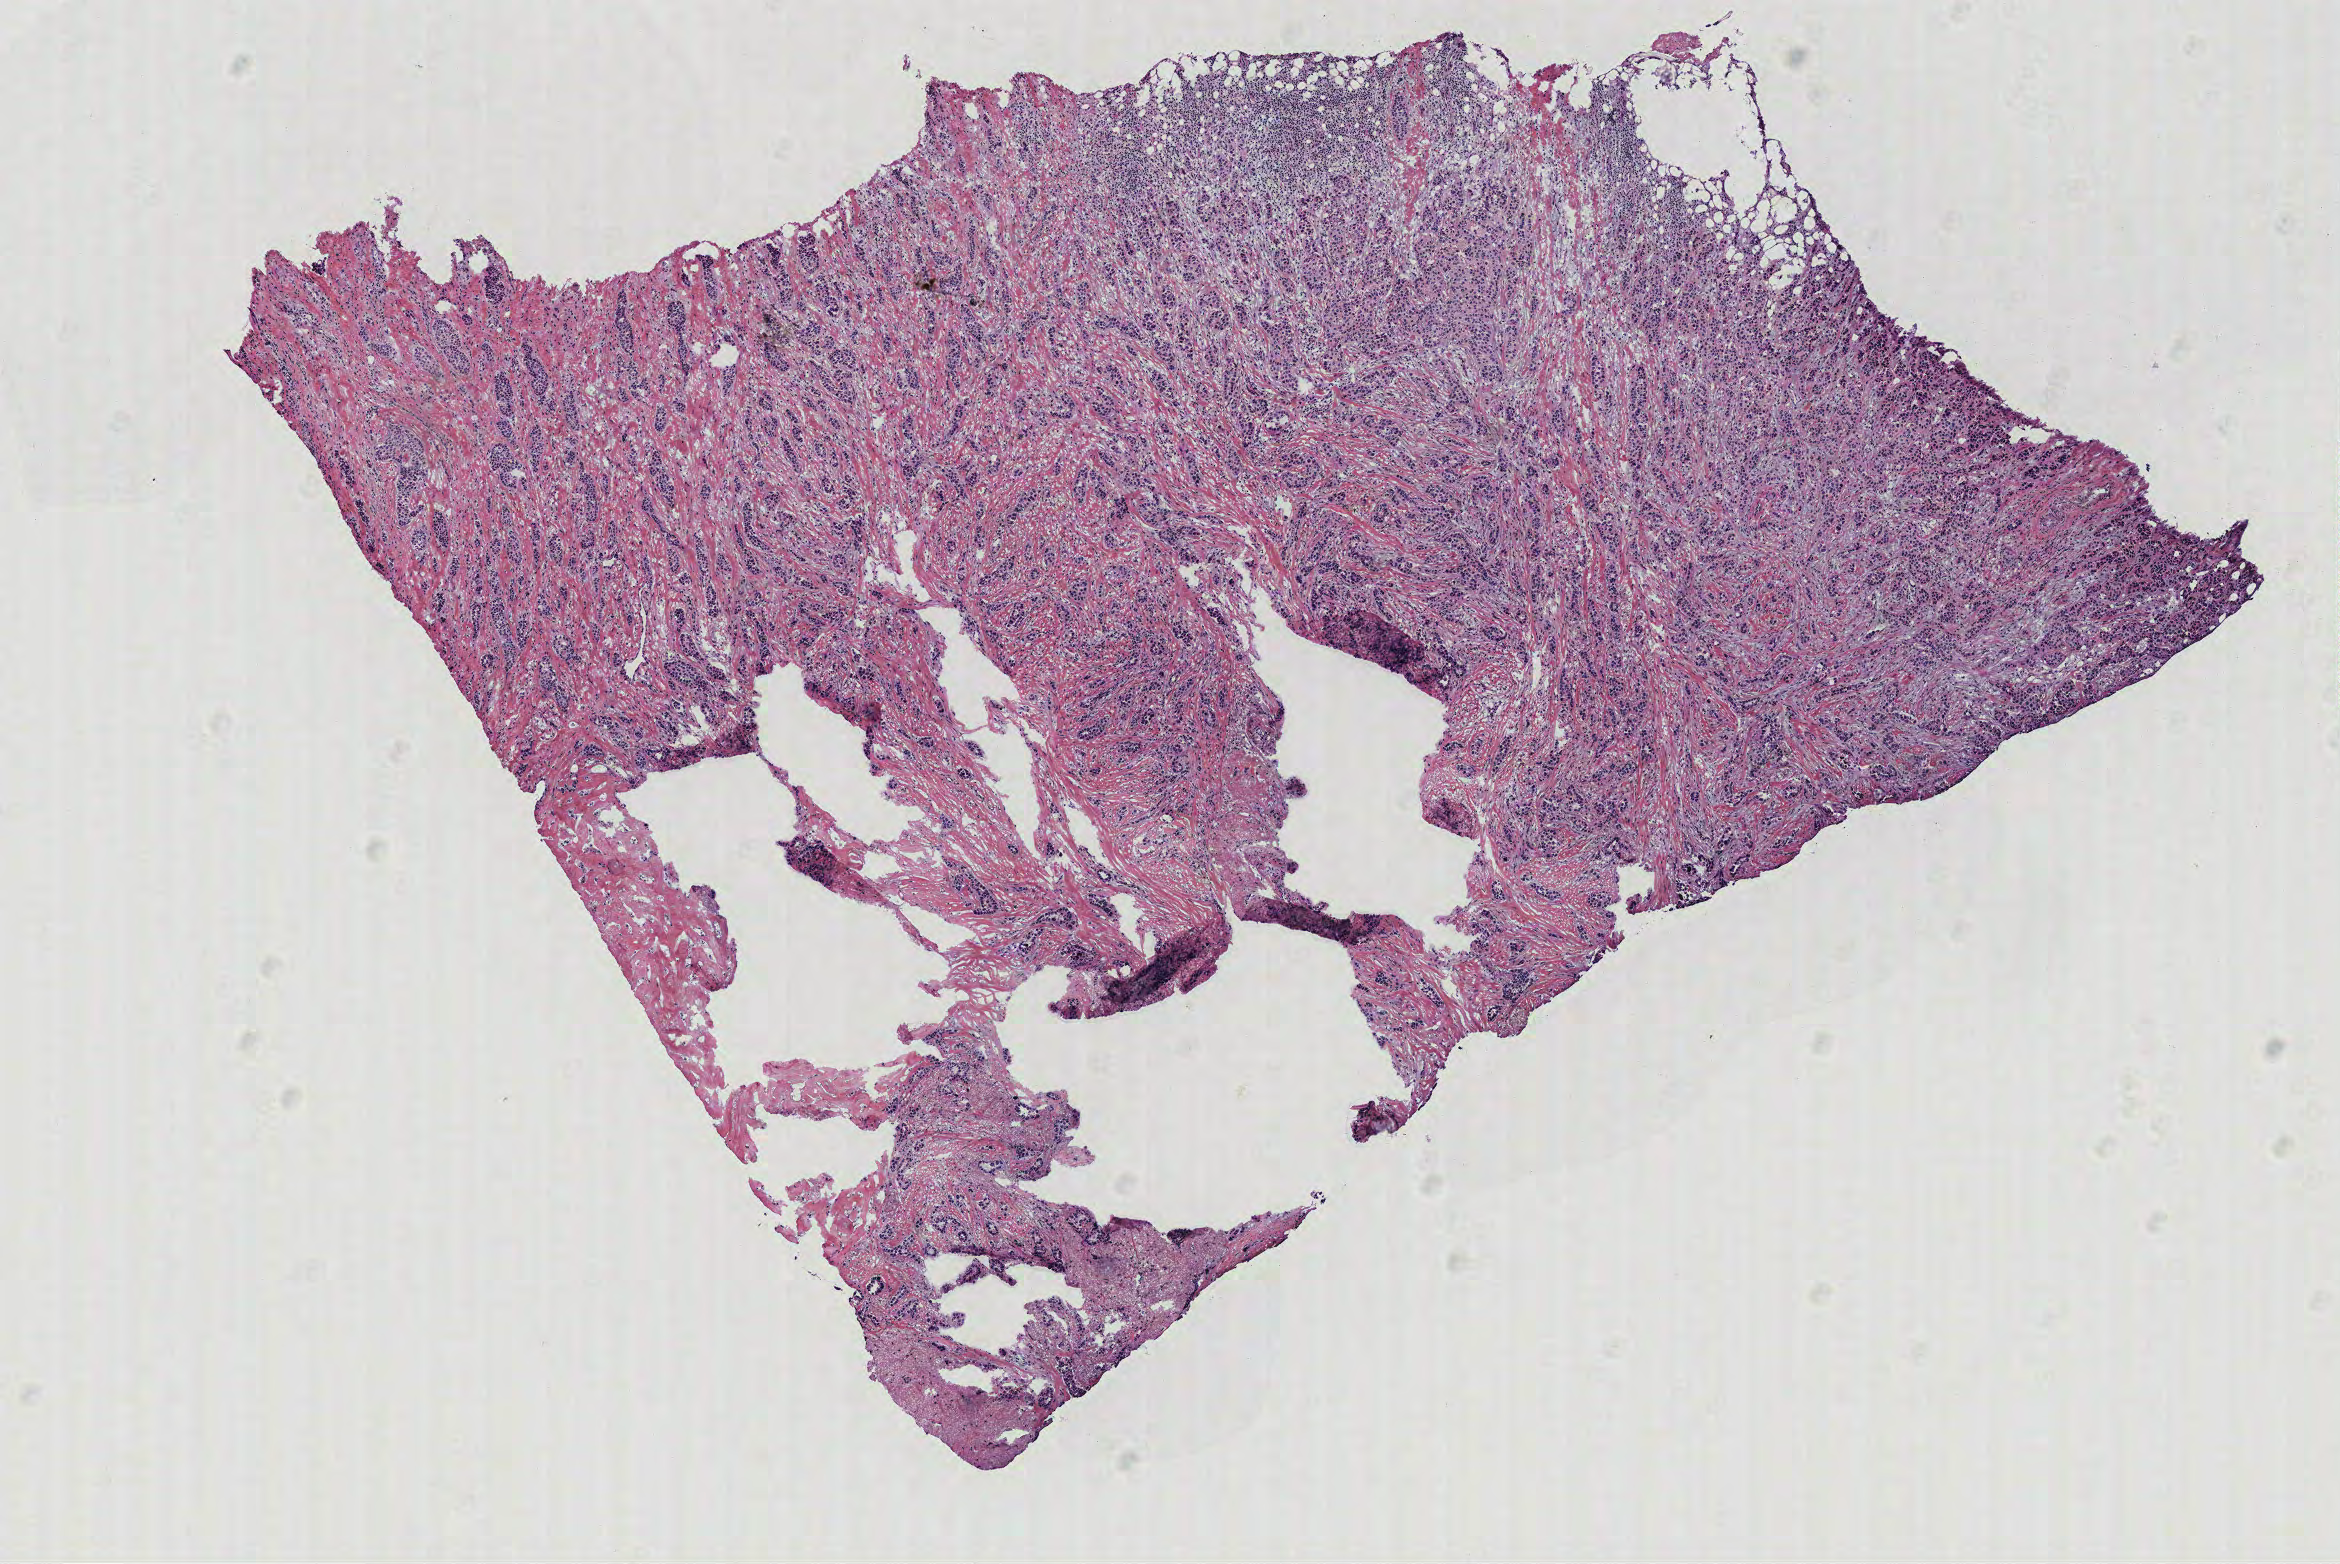
Hematoxylin and eosin (H&E) stained whole-slide image, a low-resolution overview of the entire scanned area, about 9.4 x 6.3 mm (acquisition: 40x scan); breast, tissue type not recorded.
• patient diagnosis (cohort enrolment): breast cancer (breast)